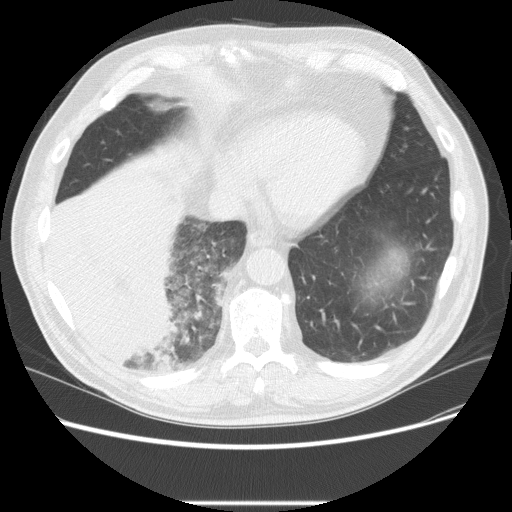
Low-dose screening chest CT, one axial slice; position 62 of 233 along the scan axis; reconstruction kernel STANDARD; 120 kVp; lung window (W 1500 / L -600 HU); 2.5 mm slice thickness; 512 × 512 image matrix, field of view 380 × 380 mm.
Annotated regions visible in this slice (outlined manually by an expert reader):
- lesion 3 (tumor, lower lobe of right lung): box from (x=48, y=196) to (x=181, y=369) px